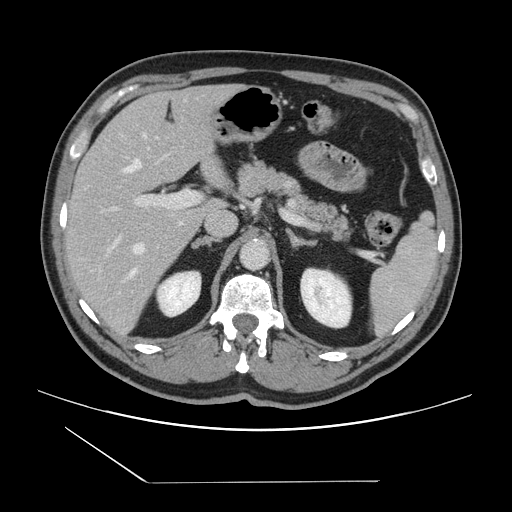
Contrast-enhanced abdominal CT, one axial slice; position 87 of 157 along the scan axis; intravenous contrast given; soft-tissue window (W 400 / L 40 HU); 2.5 mm slice thickness; 512 × 512 image matrix, field of view 407 × 407 mm. Male patient, age 61 years. Case-level facts recorded for this patient, not image findings: diagnosis: colorectal cancer liver metastases, imaged before liver resection; multiple liver metastases: yes; largest metastasis: 5.5 cm; chemotherapy before resection: no.
Outlined on this slice (manually delineated by an expert):
- hepatic veins: box from (x=122, y=133) to (x=146, y=276) px
- liver: (x=66, y=85)–(x=236, y=338)
- planned liver remnant (the part of the liver to remain after resection): (x=67, y=85)–(x=233, y=221)
- portal vein (with intrahepatic branches): (x=108, y=189)–(x=197, y=253)